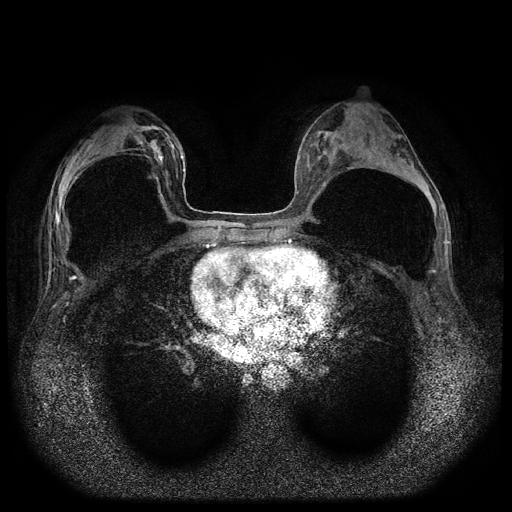
Breast MRI (dynamic contrast-enhanced, multi-phase), one axial slice. Position 43 of 116 along the scan axis. Dynamic contrast-enhanced series, time point 2 of 5 at this slice position (early post-contrast). 1.5 T. TE 2.6 ms, TR 5.4 ms. 2 mm slice thickness. 512 × 512 image matrix, field of view 340 × 340 mm. Patient: female, 42 years.
Annotated regions visible in this slice (semi-automatically segmented with operator editing):
- breast lesion (labelled 'tumour' in the annotation; benign lesions carry a separate 'benign' label): bounding box (x1, y1, x2, y2) in pixels: (150, 140, 167, 167)